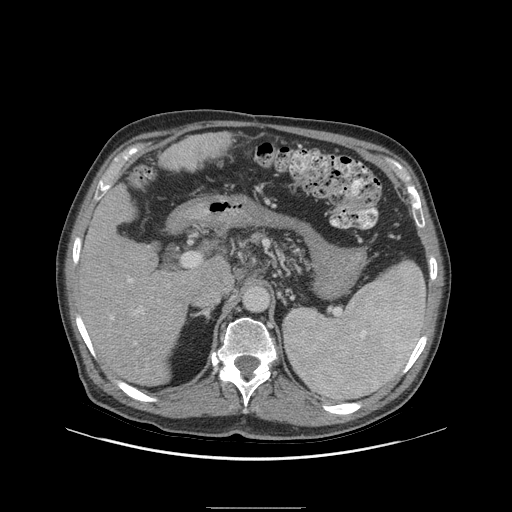
Contrast-enhanced abdominal CT (liver protocol), one axial slice. Slice 54 of 105 in the series (ordered by position). 140 kVp. Soft-tissue window (W 400 / L 40 HU). 2.5 mm slice thickness. 512 × 512 image matrix, field of view 440 × 440 mm. From the clinical record (not read from this slice): diagnosis: hepatocellular carcinoma (patient treated with transarterial chemoembolisation; whether this scan precedes or follows treatment is not stated here); TNM stage (as recorded): Stage-I; Child-Pugh class: A.
Annotated regions visible in this slice (semi-automatic segmentation, software-assisted and operator-edited):
- liver parenchyma outside the tumour (the mass and vessels are separate outlines, so this box may not span the whole liver): bounding box <74,185,200,386> (left, top, right, bottom; pixels)
- liver vessels: <92,278,140,354>